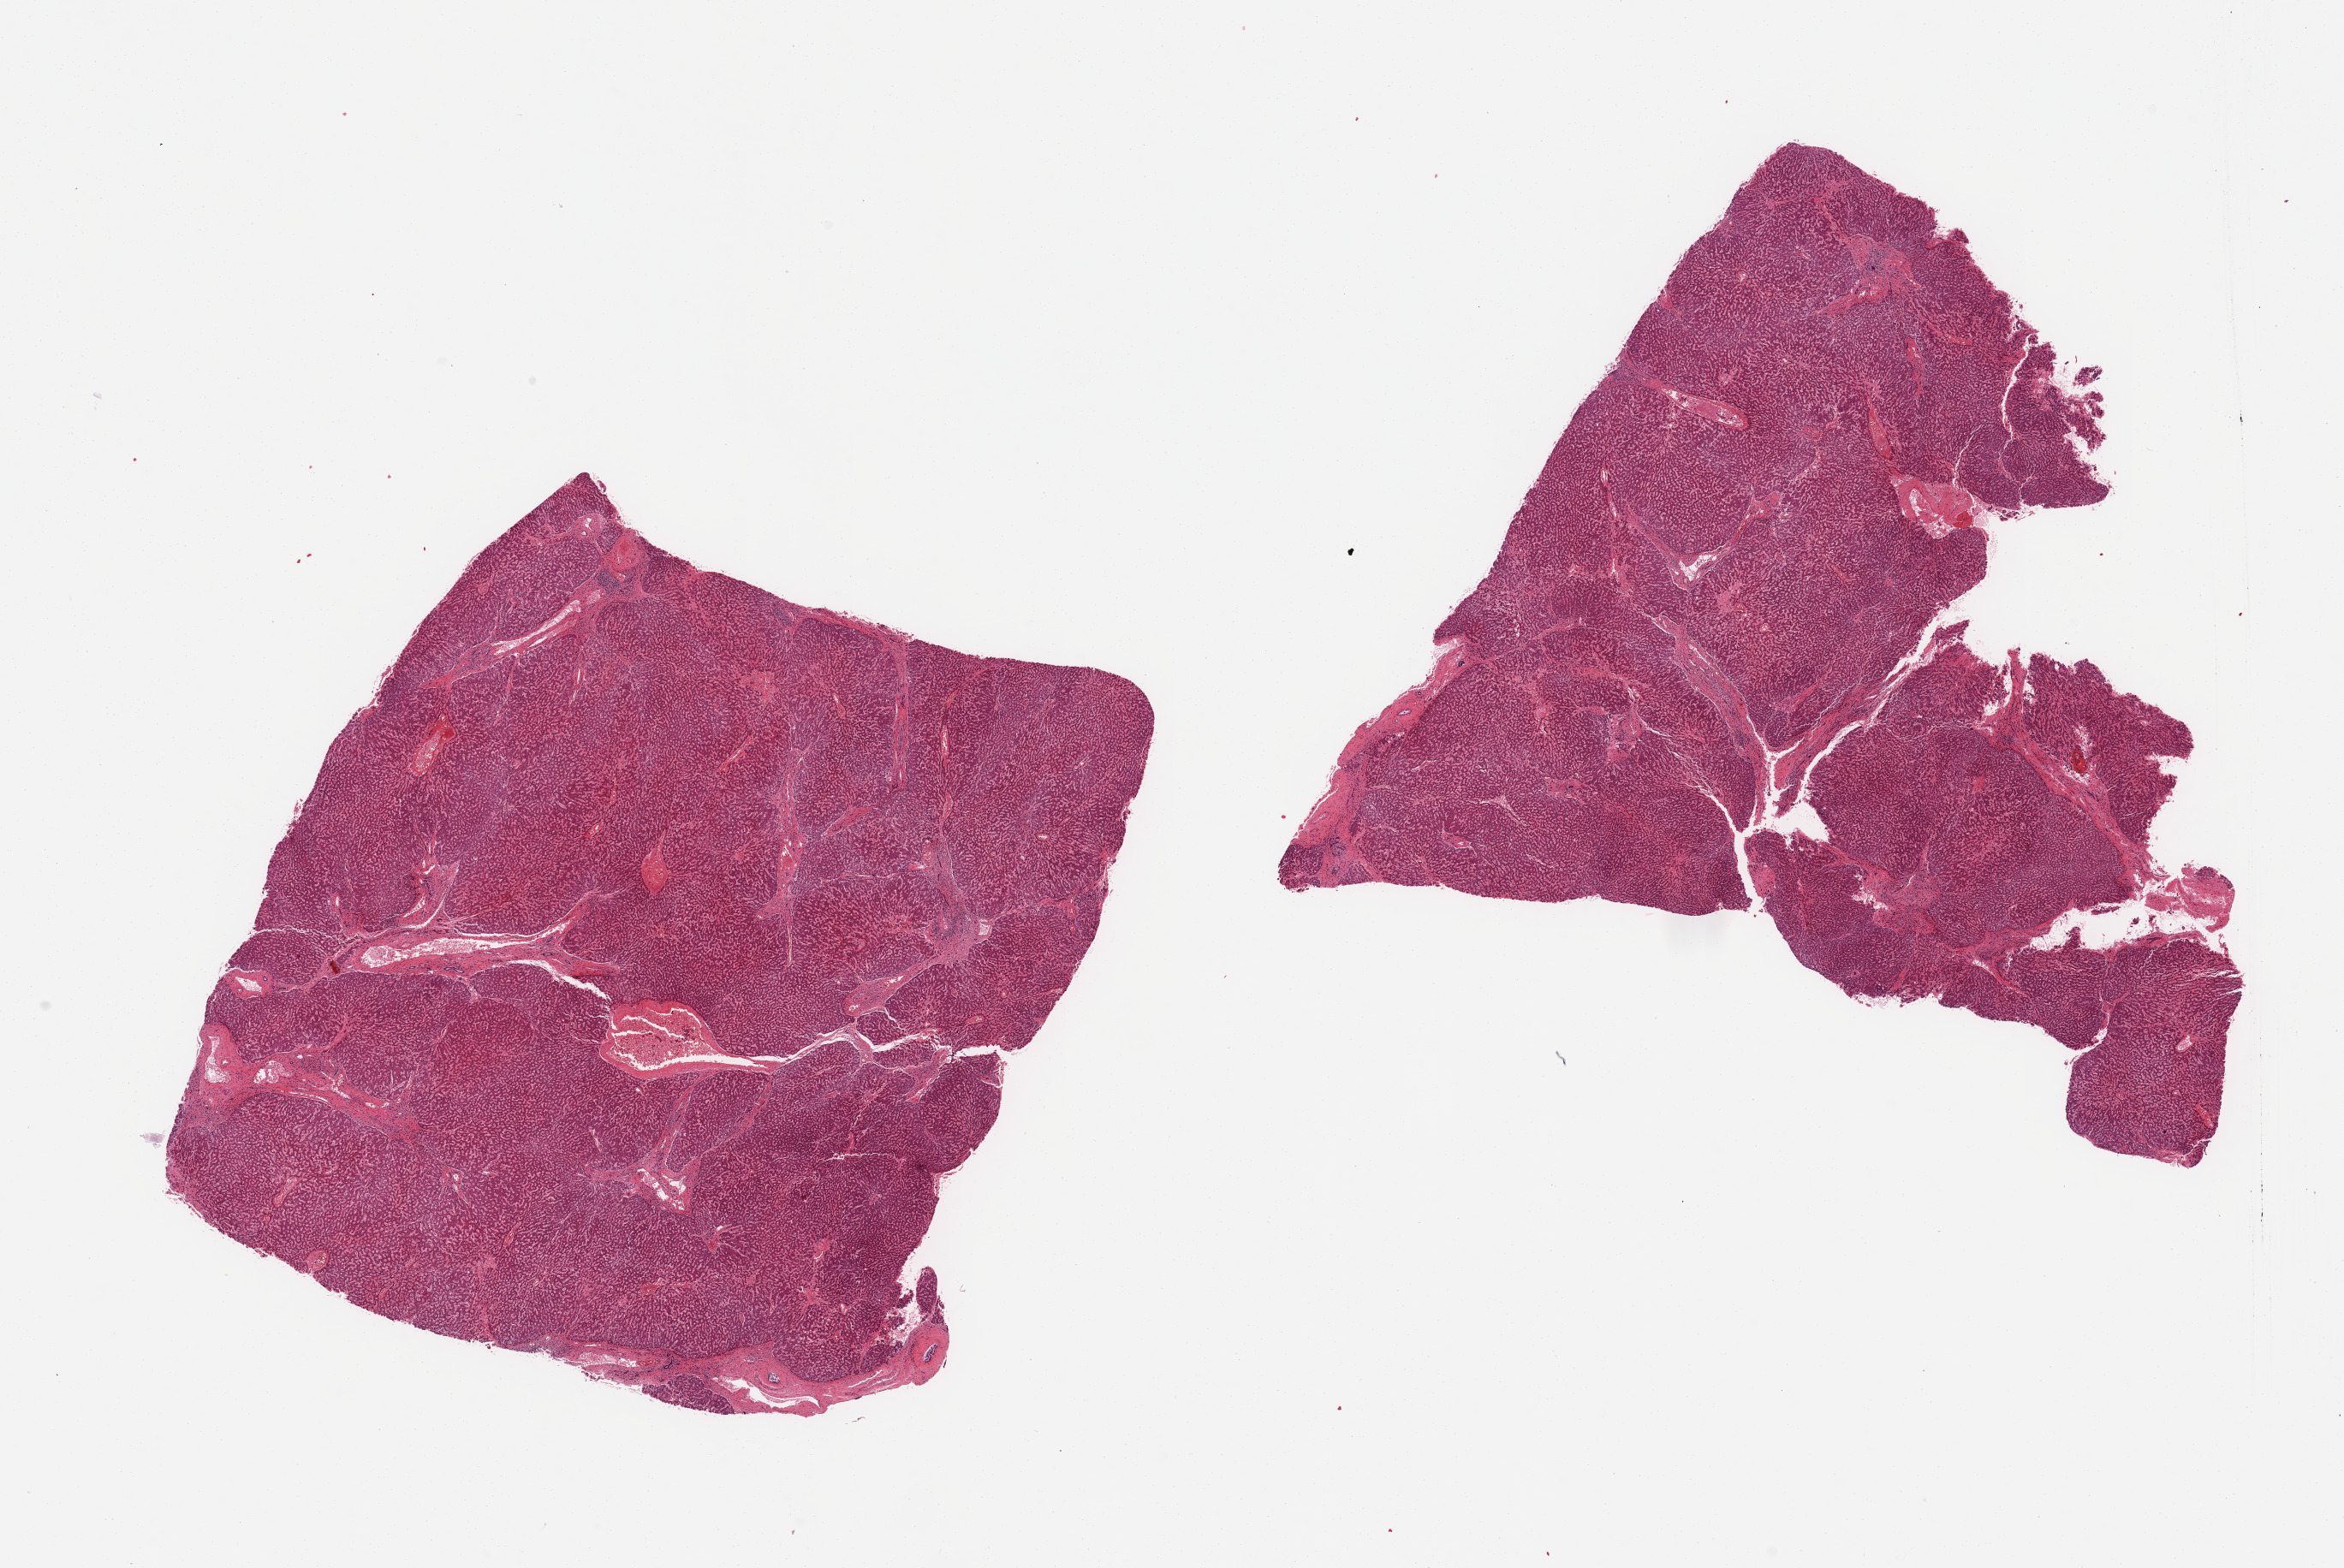
Hematoxylin and eosin (H&E) whole-slide image — a low-resolution overview of the entire scanned area, about 21.7 x 14.5 mm; PAXgene-fixed, paraffin-embedded tissue; sampled site (target tissue): liver; donor tissue sample. Female donor.
Reviewer comment on this tissue sample: 2 pieces; mild mainly periportal macrosteatosis.